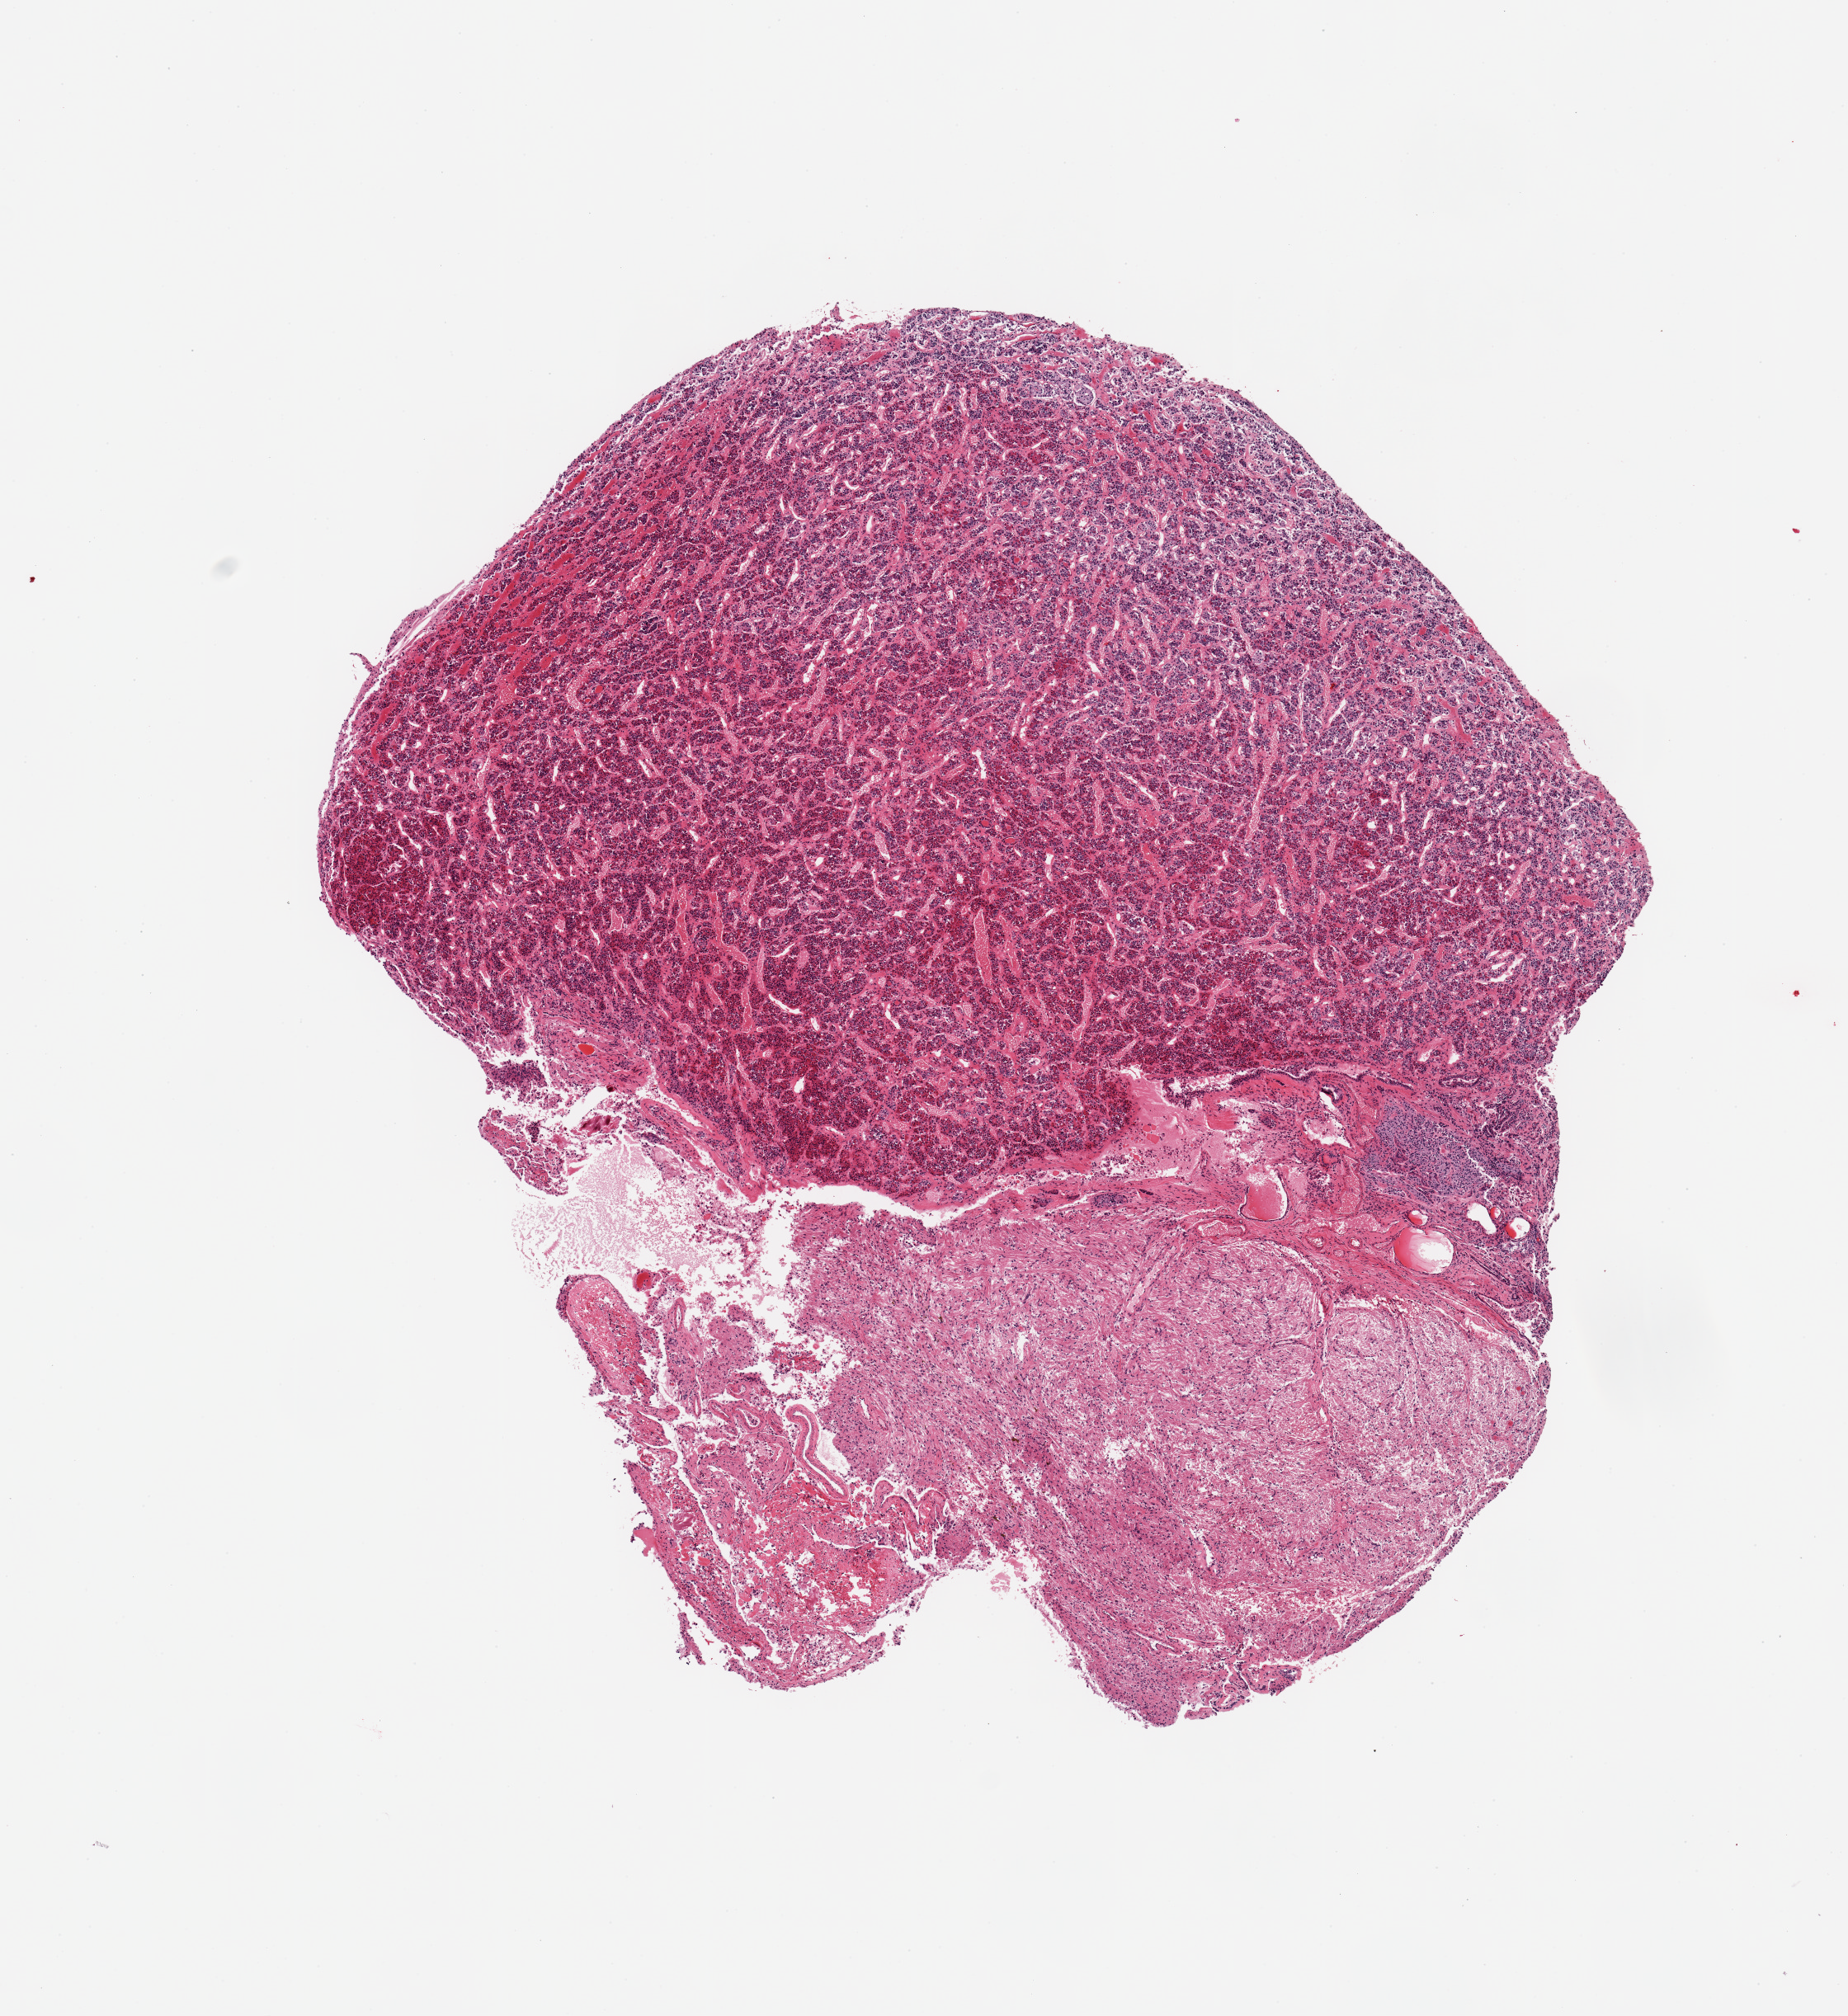
Whole-slide image, H&E stain, brightfield — whole scanned area (about 8.9 x 9.7 mm, slide scanned at 20x) shown as a low-resolution overview, PAXgene-fixed paraffin-embedded (PFPE) section, target tissue: pituitary, tissue donor sample. Donor sex: male.
* pathologist's review note for this sample: 1 piece; 60% adenohypophysis and 40% neurohypophysis